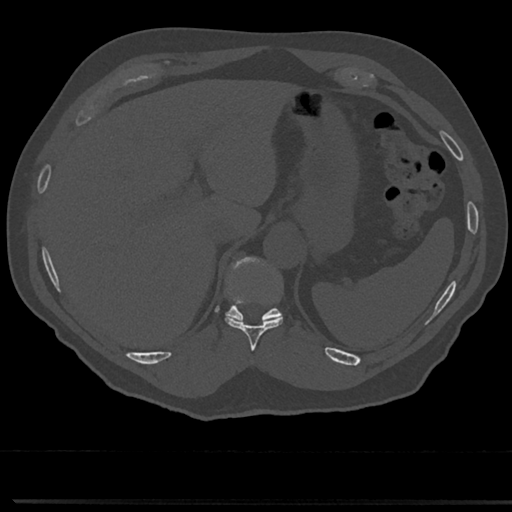
CT including the spine, one axial slice. Position 237 of 817 along the scan axis. 120 kVp. Bone window (W 1800 / L 400 HU). 512 × 512 image matrix. Male patient, age 61 years. From the clinical record (not read from this slice): primary cancer: prostate.
Annotated regions visible in this slice (semi-automatic segmentation, software-assisted and operator-edited):
- T10 vertebra: bounding box <225,273,283,349> (left, top, right, bottom; pixels)
- T11 vertebra: <227,260,281,322>